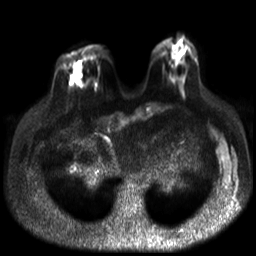
Breast MRI, one axial slice. Position 11 of 30 along the scan axis. Diffusion-weighted series; image 2 of 4 stored at this slice position (different b-values; order by instance number). 3 T. 4 mm slice thickness. 256 × 256 image matrix, field of view 320 × 320 mm. Female patient.
Annotated regions visible in this slice (manually delineated by an expert):
- tumour on diffusion-weighted imaging: bounding box [x1, y1, x2, y2] px = [70, 74, 82, 86]